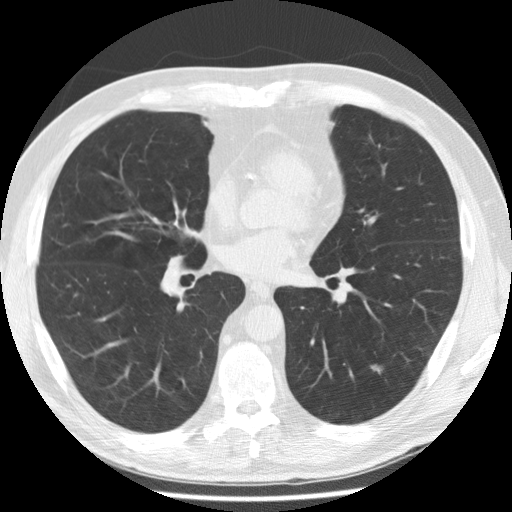
Axial slice from a low-dose chest CT screening exam; second screening round (one year after baseline); lung window (W 1500 / L -600 HU); 120 kVp. Male, age 58 years at enrolment. Former smoker at enrolment.
- Expert-annotated lung lesion, bounding box <357,351,394,385> (left, top, right, bottom; pixels).
- The exam's reader record, not a measurement of the box and not confirmed to be the same lesion: non-calcified nodule or mass ≥4 mm, left lower lobe, 7 × 4 mm, poorly defined margins, ground glass attenuation, pre-existing on the prior screen: yes; interval growth: yes.
- Later outcome: lung cancer diagnosed 407 days after this screen — adenocarcinoma, NOS, left lower lobe, poorly differentiated (G3), stage IA (AJCC 6th edition), 8 mm at pathology.